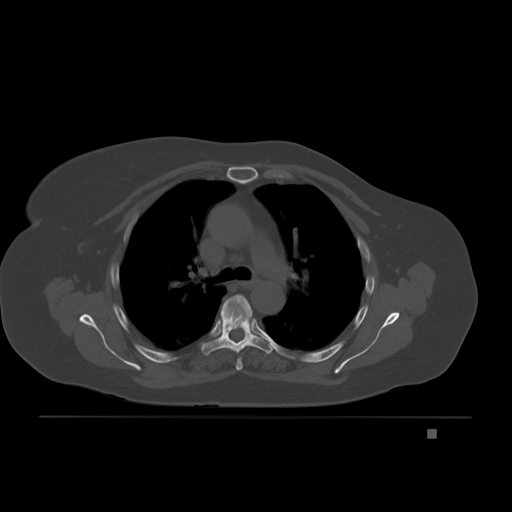
CT including the spine, one axial slice; position 147 of 221 along the scan axis; bone window (W 1800 / L 400 HU); 3 mm slice thickness; 512 × 512 image matrix, field of view 474 × 474 mm. Patient: female, 63 years. Case-level facts recorded for this patient, not image findings: primary cancer: breast.
Annotated regions visible in this slice (semi-automatically segmented with operator editing):
- T4 vertebra: bounding box (x1, y1, x2, y2) in pixels: (236, 327, 250, 370)
- T5 vertebra: (201, 295, 272, 356)